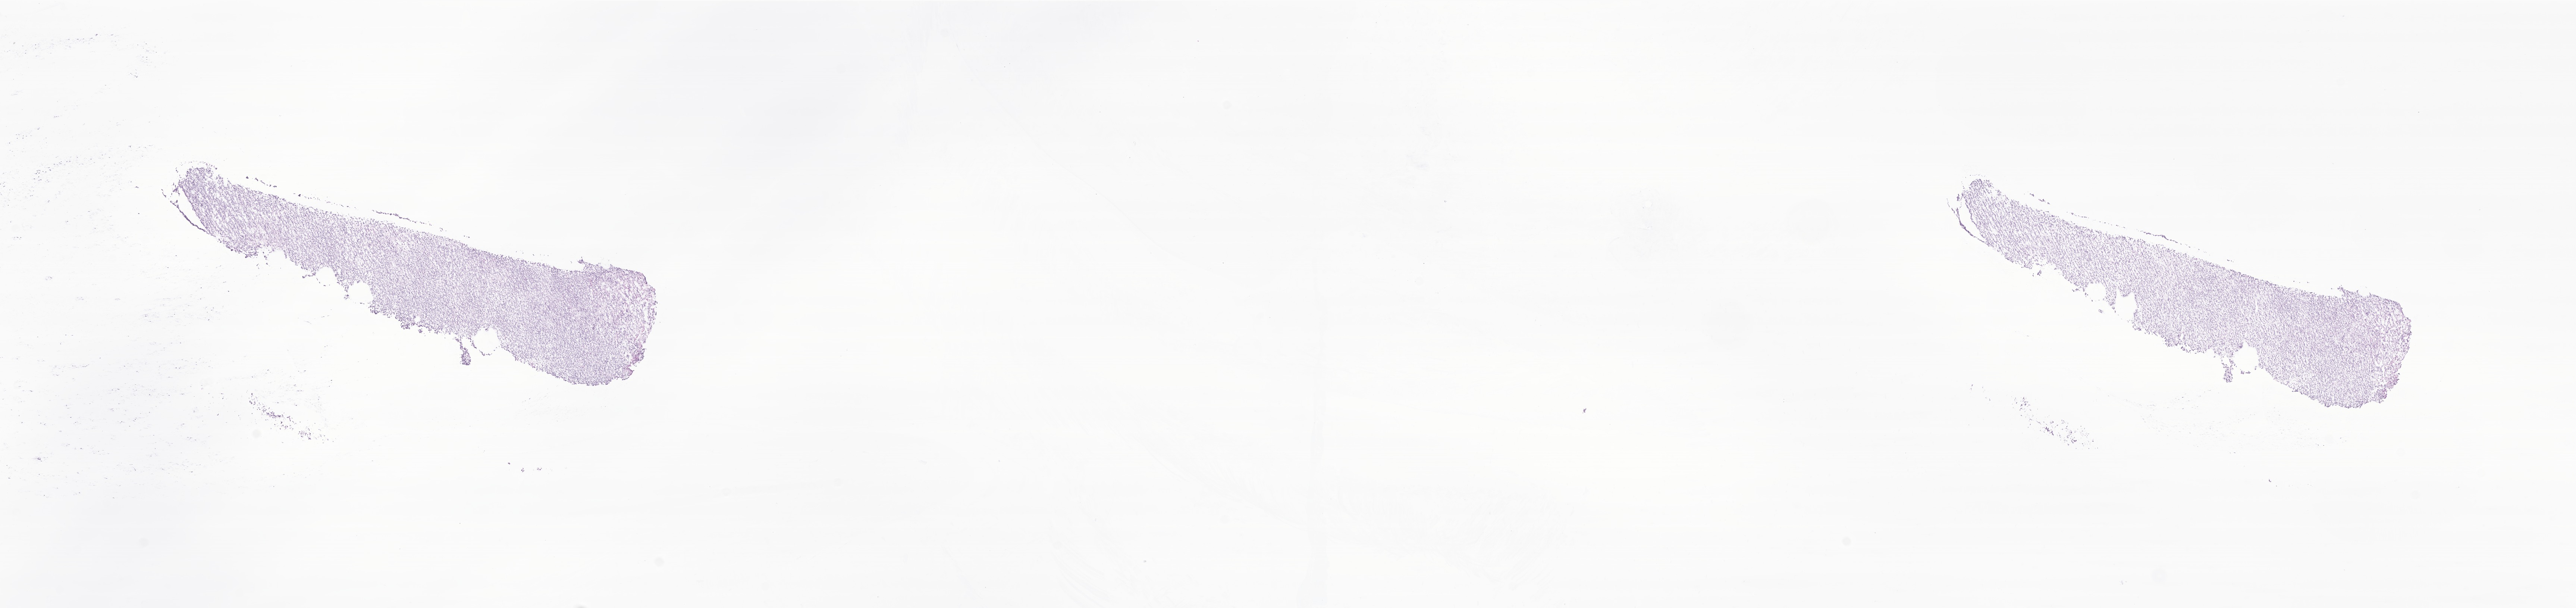
H&E whole-slide image of tumor tissue from the cerebral ventricle, low-resolution overview of the scanned area, about 29.1 x 6.9 mm, frozen section. Patient male; age 138 months (11 years 6 months).
Recorded diagnosis: Medulloblastoma, NOS.